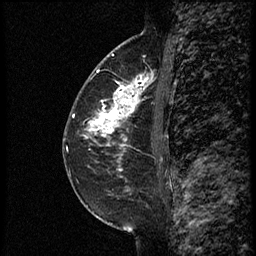
Breast MRI (dynamic contrast-enhanced), one sagittal slice; slice 35 of 60 in the series (ordered by position); dynamic contrast-enhanced study with each time point stored as its own series, time point 2 of 3 at this slice position (early post-contrast, ordered by acquisition time); 1.5 T; TE 4.2 ms, TR 18.9 ms; 256 × 256 image matrix, field of view 200 × 200 mm. Female patient. Case-level facts recorded for this patient, not image findings: setting: breast cancer imaged before/during neoadjuvant chemotherapy; receptor status: HER2-positive.
Annotated regions visible in this slice (semi-automatic segmentation, software-assisted and operator-edited):
- analysis volume of interest (the breast-tissue region the enhancement analysis was run in; not a lesion): bounding box (x1, y1, x2, y2) in pixels: (85, 67, 161, 147)
- tumour enhancement mask (voxels above the 100 % enhancement threshold inside the analysis volume of interest): (91, 75, 150, 147)